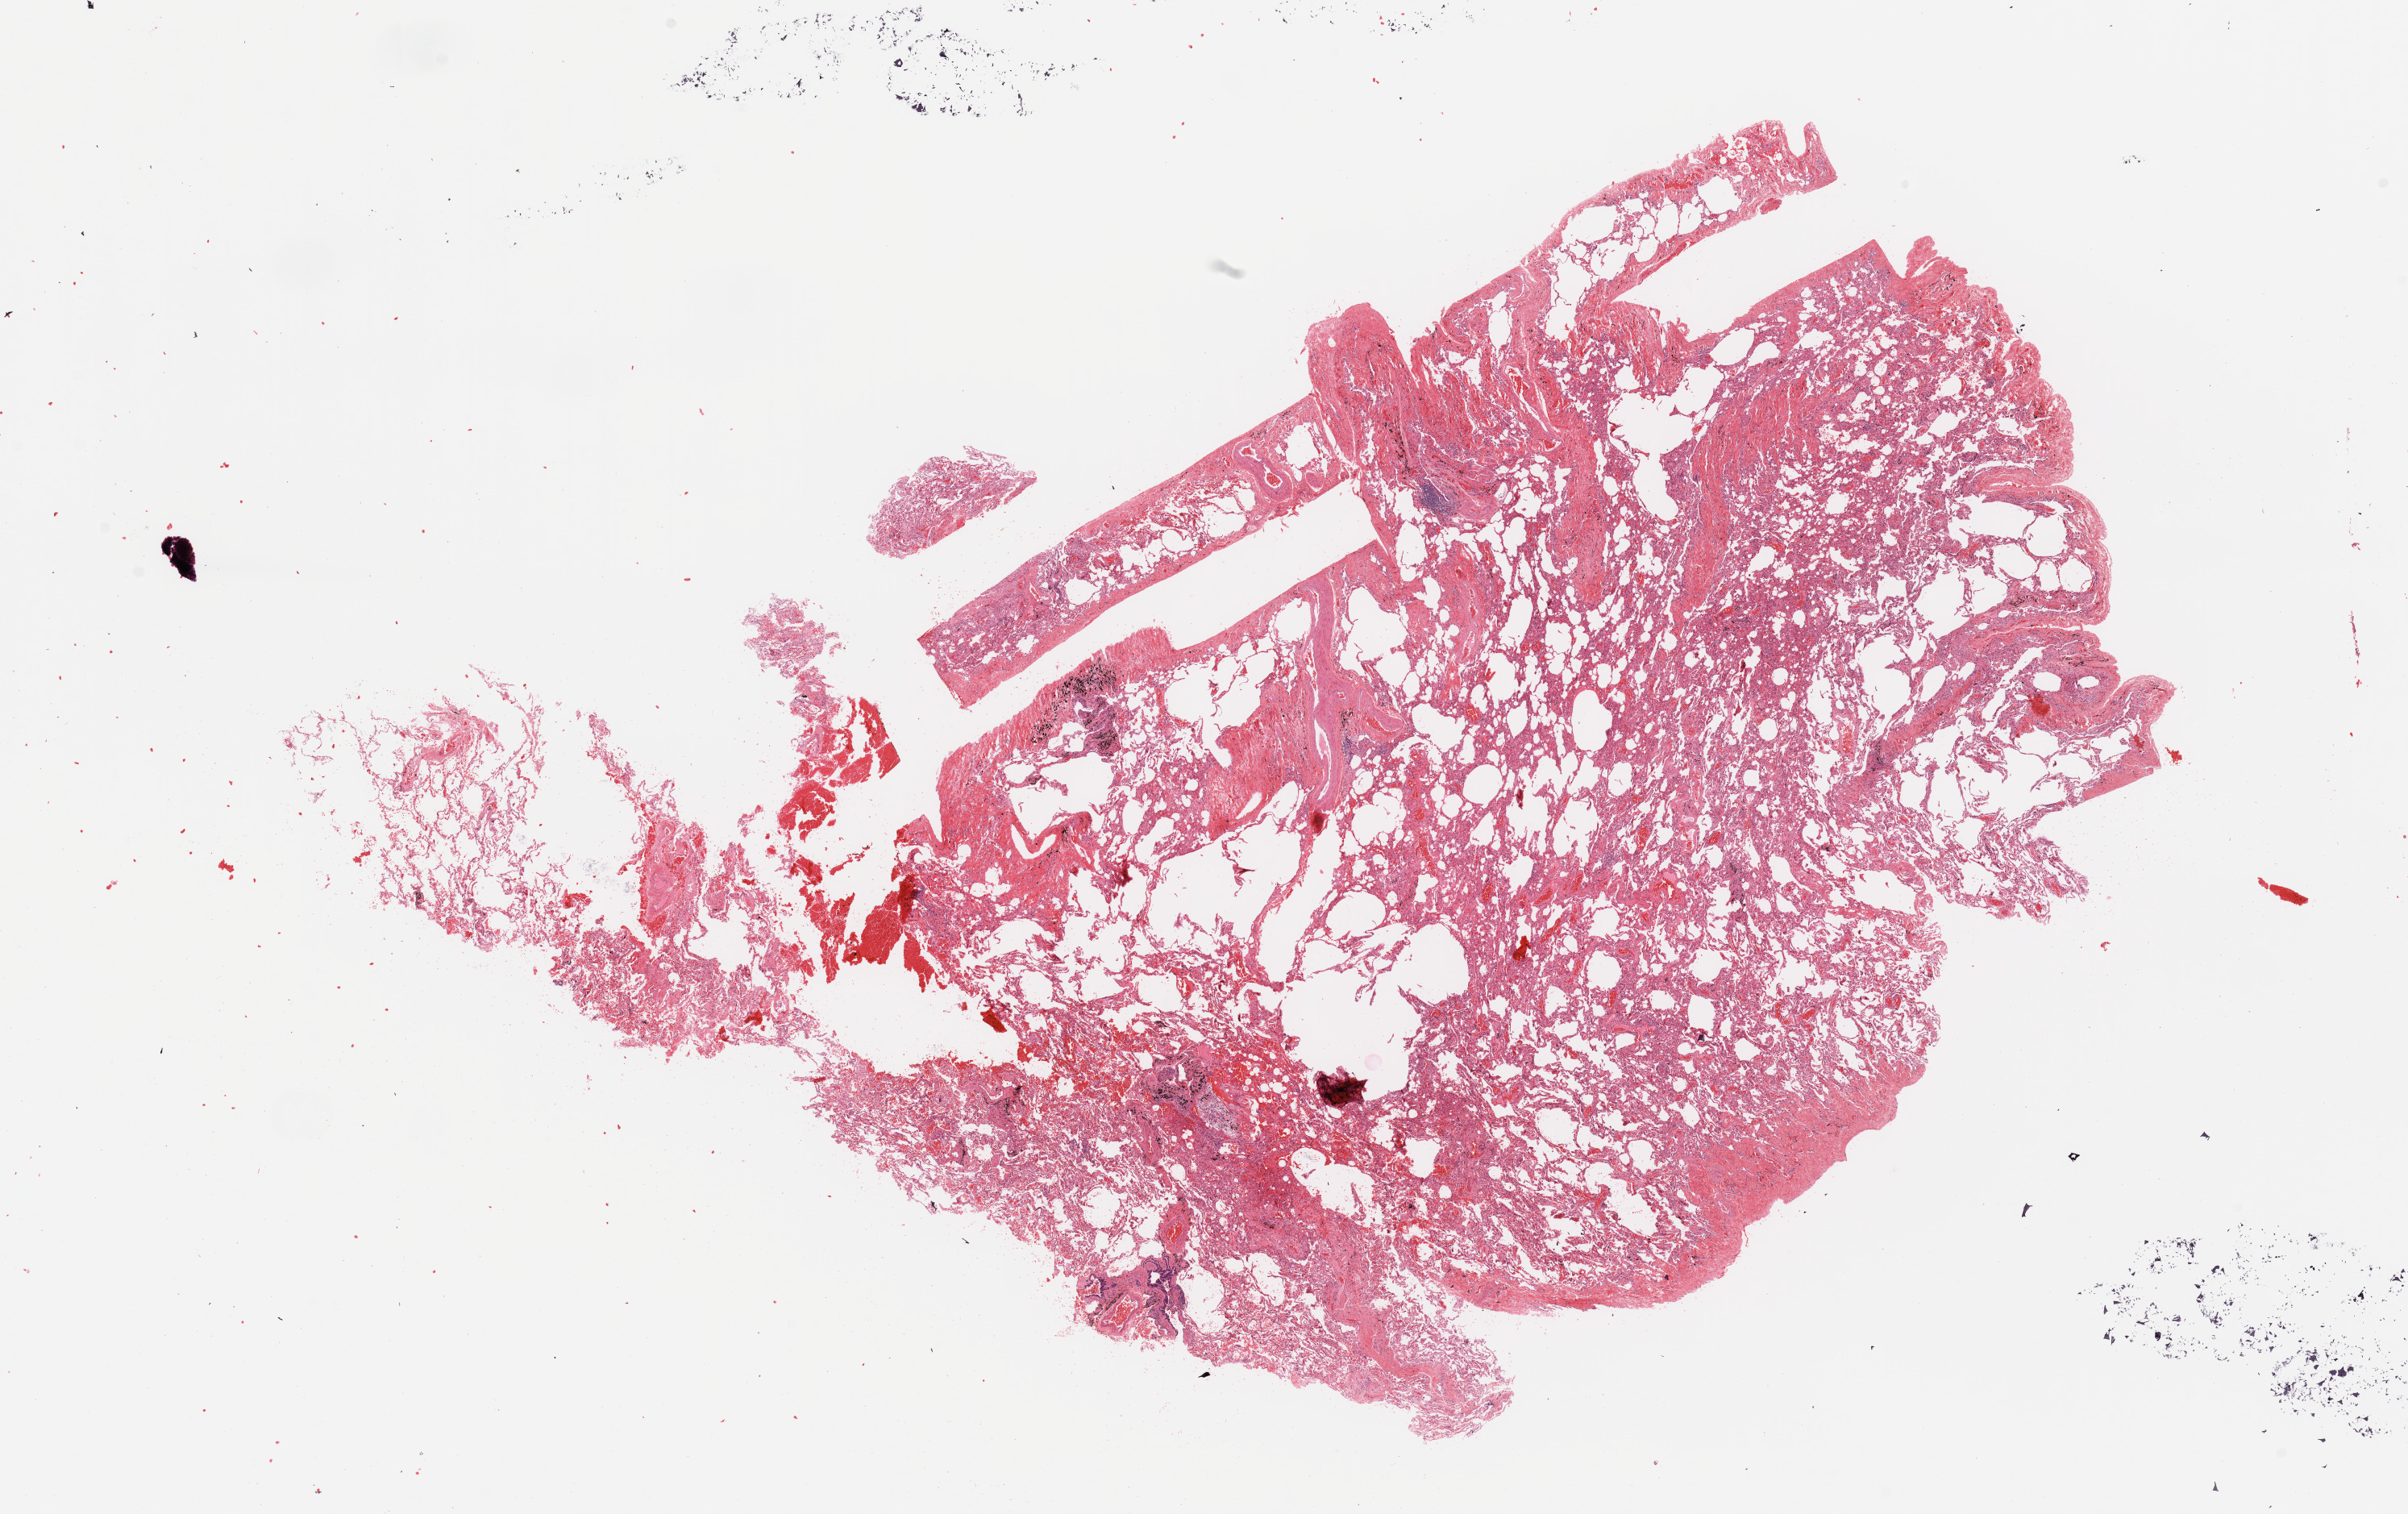
H&E whole-slide image — whole scanned area (about 23.6 x 14.9 mm) shown as a low-resolution overview; normal (non-tumour) tissue sample, sampled site: lung. Male, 45 y/o.
* this section: normal (non-tumour) tissue from the same patient
* patient diagnosis: Adenocarcinoma, NOS